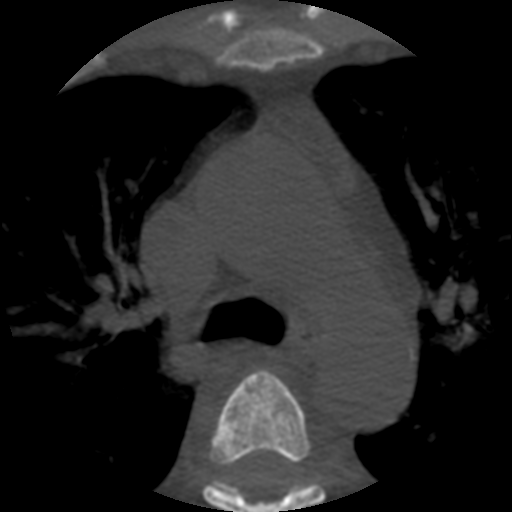
CT including the spine, one axial slice; reconstruction kernel STANDARD; 120 kVp; bone window (W 1800 / L 400 HU); 1.25 mm slice thickness; 512 × 512 image matrix, field of view 160 × 160 mm. Patient age 57 years. From the clinical record (not read from this slice): primary cancer: prostate.
Outlined on this slice (semi-automatically segmented with operator editing):
- T4 vertebra: bounding box <203,371,326,512> (left, top, right, bottom; pixels)
- T5 vertebra: <211,480,315,495>